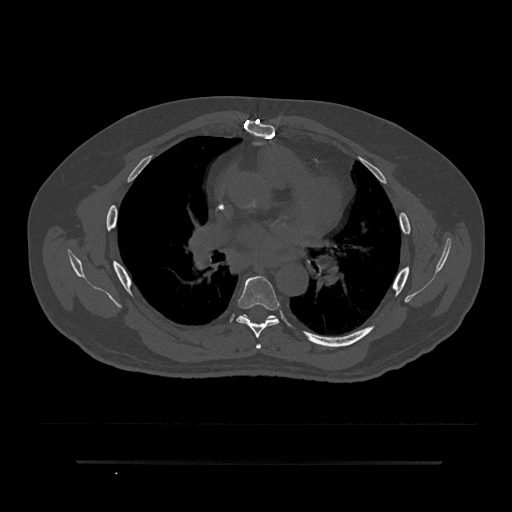
CT including the spine, one axial slice; slice 518 of 797 in the series (ordered by position); reconstruction kernel Br40s/3; 120 kVp; bone window (W 1800 / L 400 HU); 0.5 mm slice thickness; 512 × 512 image matrix, field of view 464 × 464 mm. Patient: male, 59 years. Case-level facts recorded for this patient, not image findings: primary cancer: bile ducts.
Annotated regions visible in this slice (semi-automatic segmentation, software-assisted and operator-edited):
- T5 vertebra: bounding box [x1, y1, x2, y2] px = [256, 344, 262, 349]
- T6 vertebra: [236, 276, 281, 338]